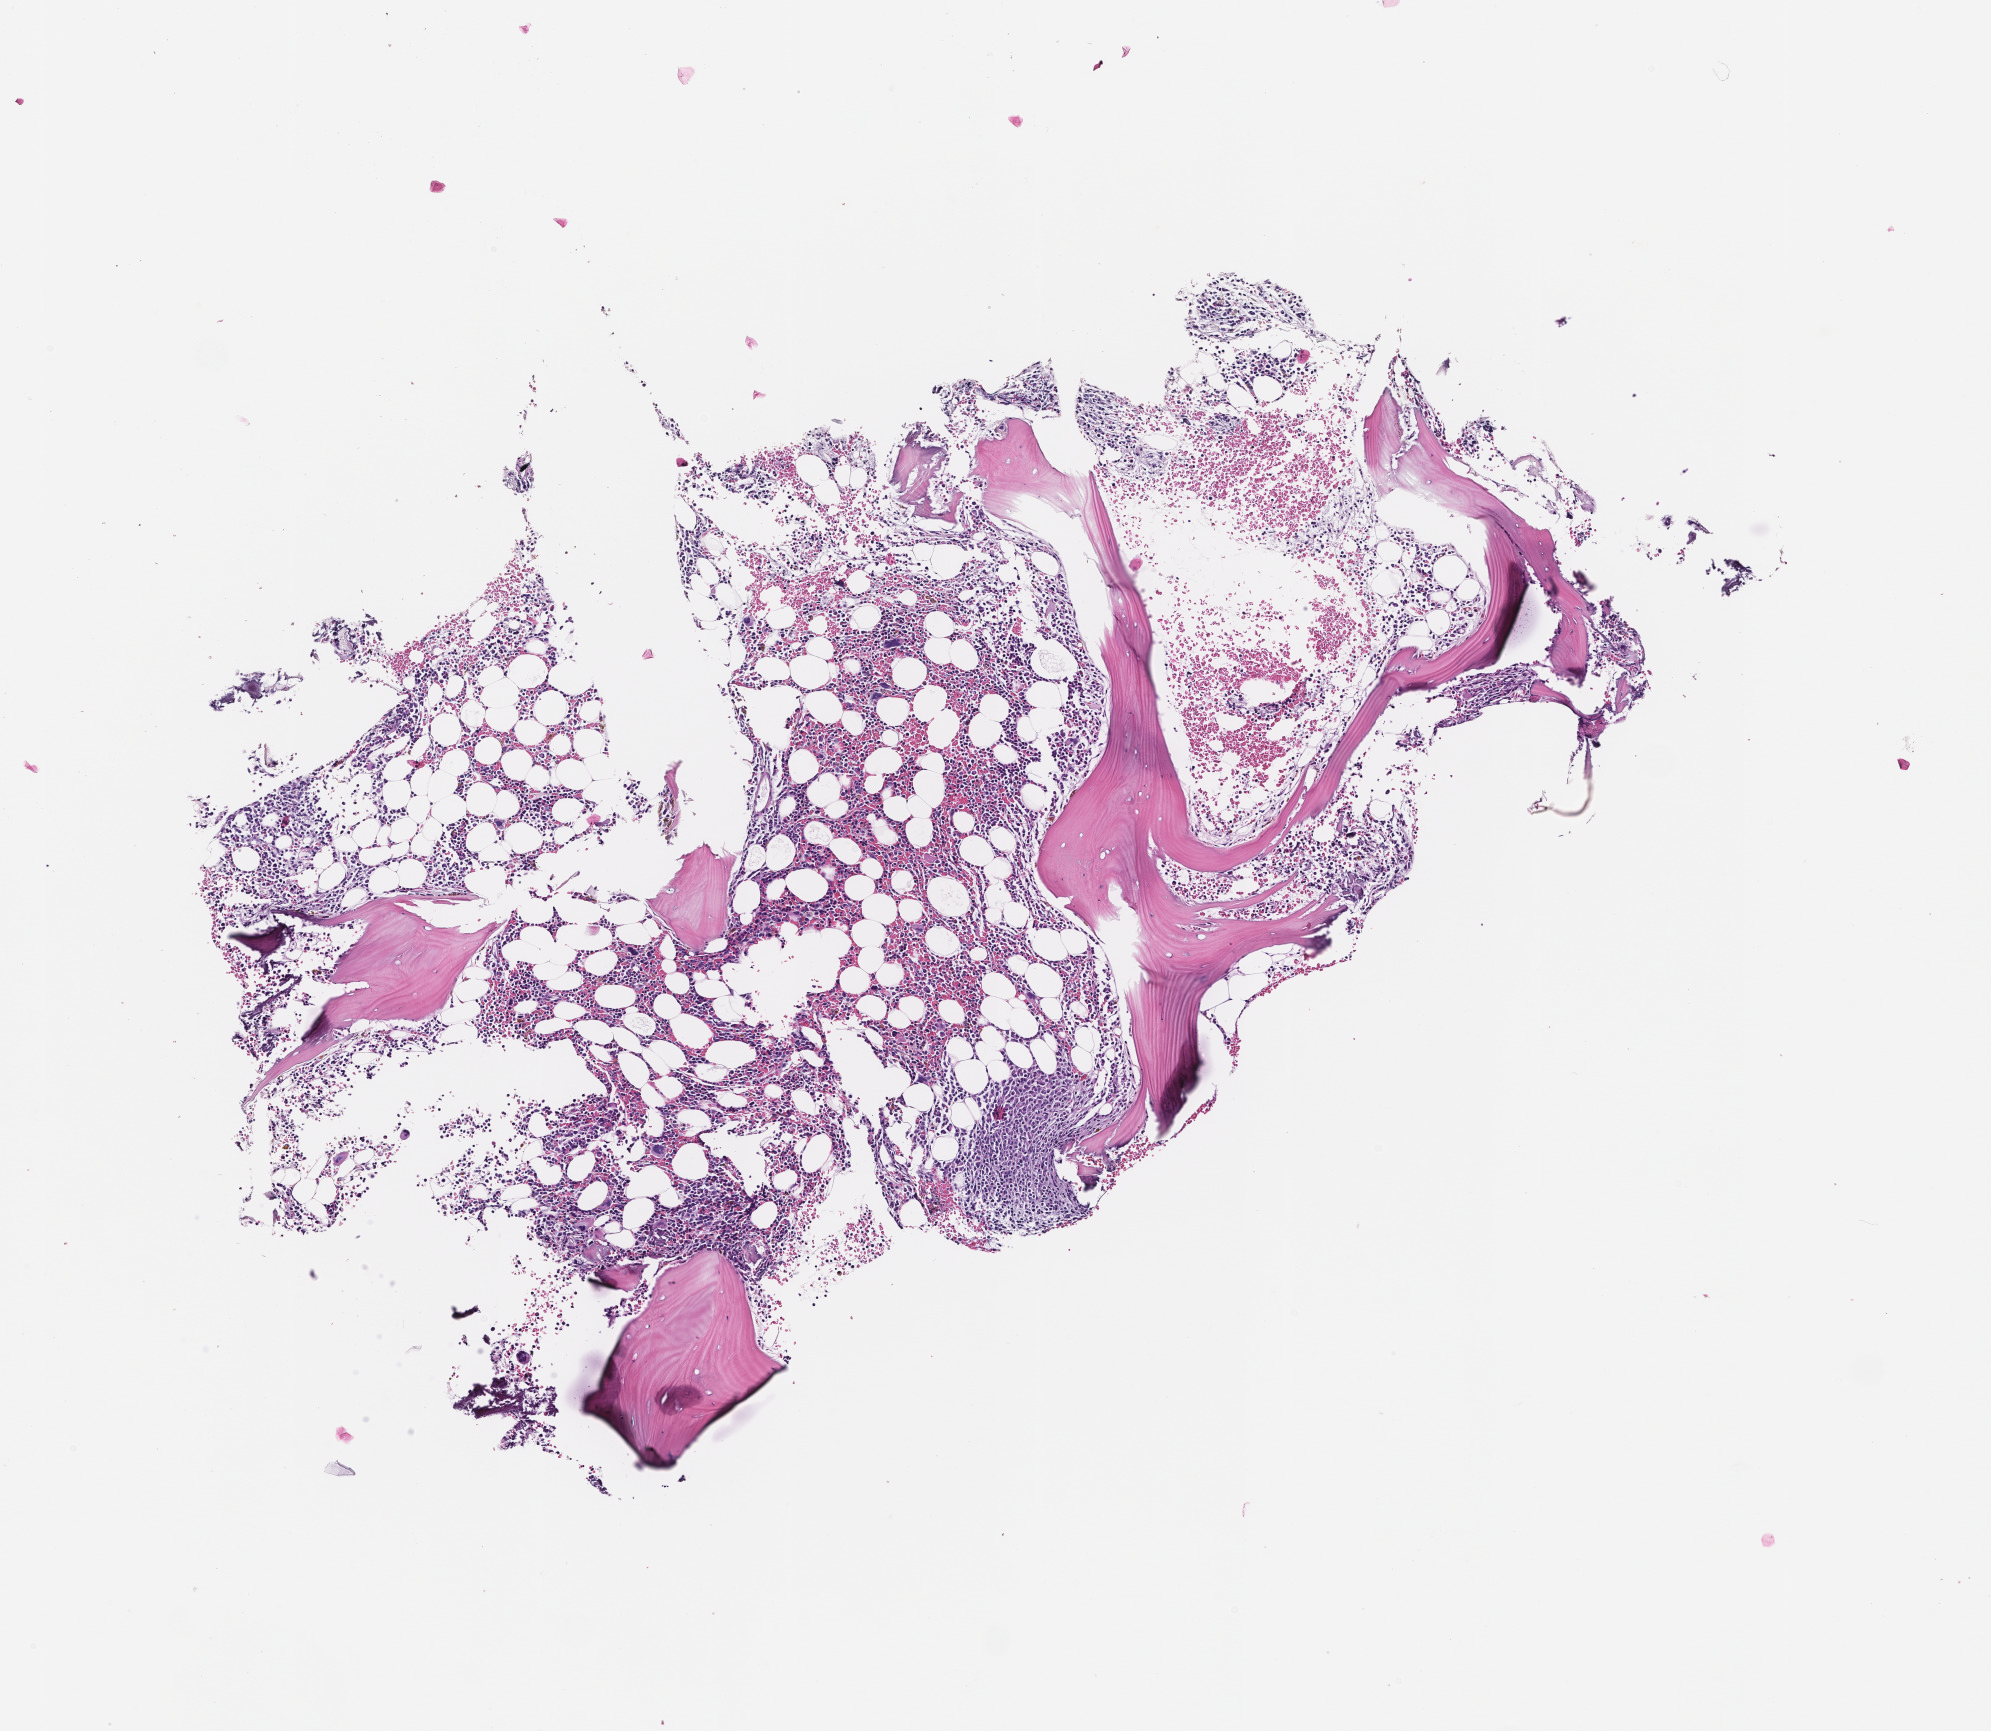
H&E whole-slide image, shown as a low-resolution overview of the whole scanned area (about 4.0 x 3.5 mm), formalin-fixed paraffin-embedded section, site: bone marrow. Patient sex: male.
* this section: primary tumor
* diagnosis: Plasma Cell Myeloma